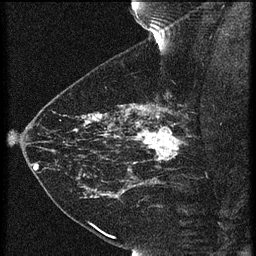
Breast MRI (dynamic contrast-enhanced), one sagittal slice; position 46 of 60 along the scan axis; 3 images stored at this slice position (order not interpretable as contrast timing); 1.5 T; TE 4.2 ms, TR 21.3 ms; 1.5 mm slice thickness; 256 × 256 image matrix, field of view 180 × 180 mm. Patient: female, 43 years. Case-level facts recorded for this patient, not image findings: setting: breast cancer imaged before/during neoadjuvant chemotherapy; receptor status: HER2-positive.
Structures marked on this image (semi-automatically segmented with operator editing):
- analysis volume of interest (the breast-tissue region the enhancement analysis was run in; not a lesion): box from (x=119, y=114) to (x=189, y=173) px
- tumour enhancement mask (voxels above the 90 % enhancement threshold inside the analysis volume of interest): (x=119, y=114)–(x=182, y=163)